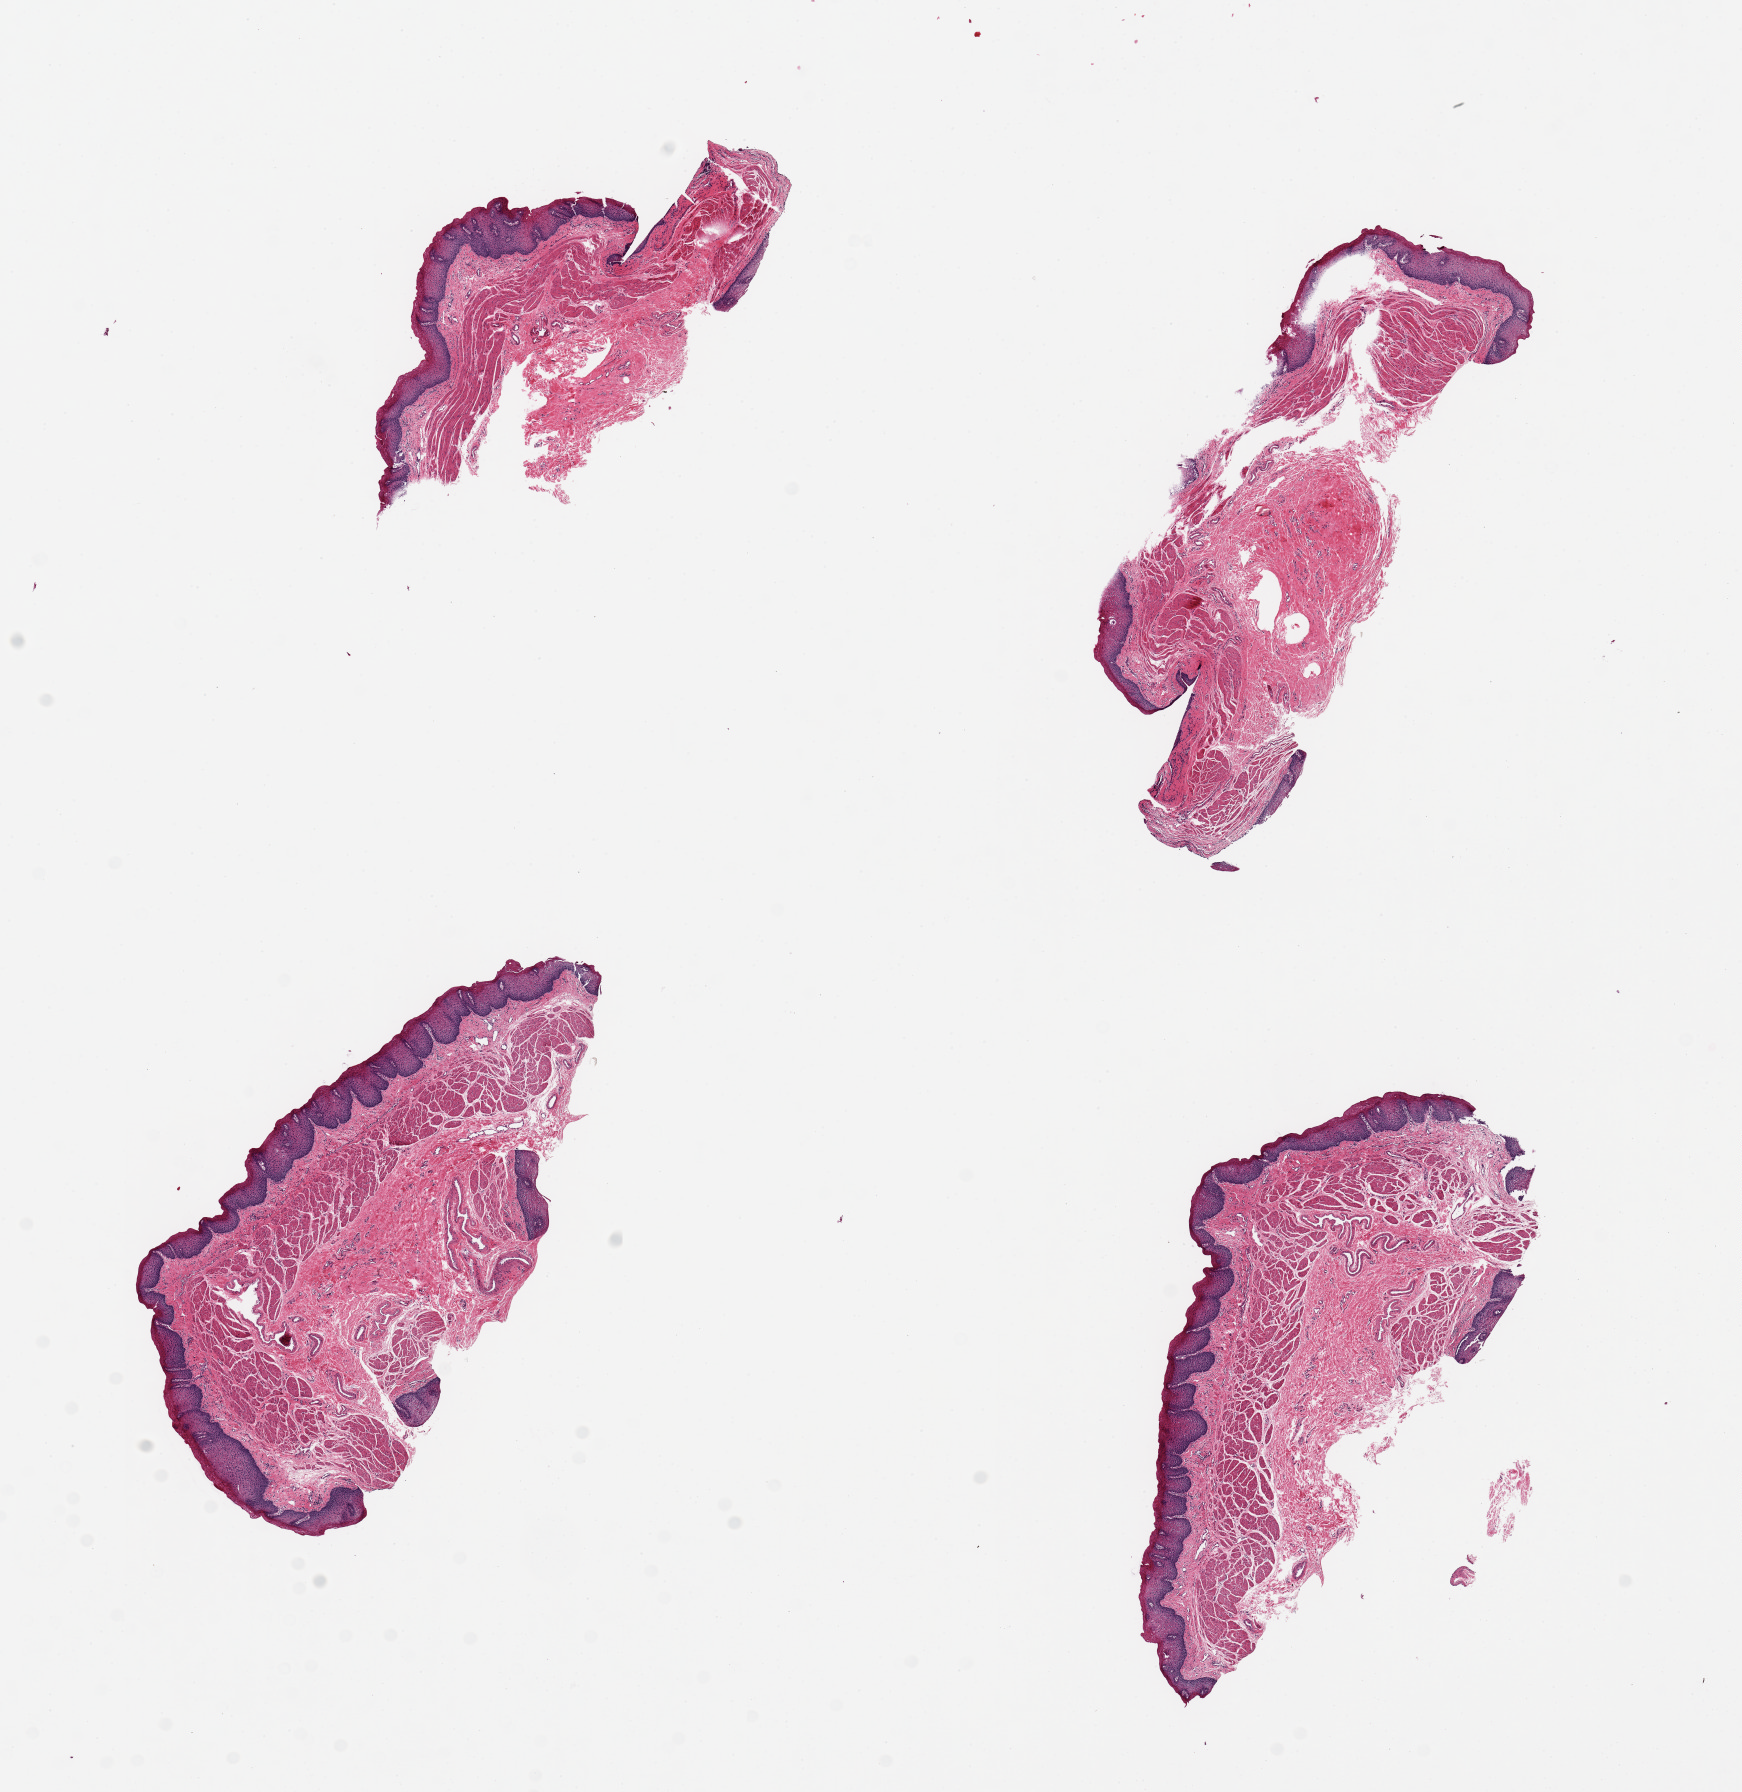
Digitized haematoxylin and eosin-stained section, a low-resolution overview of the entire scanned area, about 13.8 x 14.2 mm (acquisition: 20x scan), PAXgene-fixed paraffin-embedded (PFPE) section, target tissue: esophageal mucous membrane, tissue donor sample. Male donor.
• review note (as recorded): 4 pieces; eosinophilic squamous surface may indicate strong alcohol ingestion